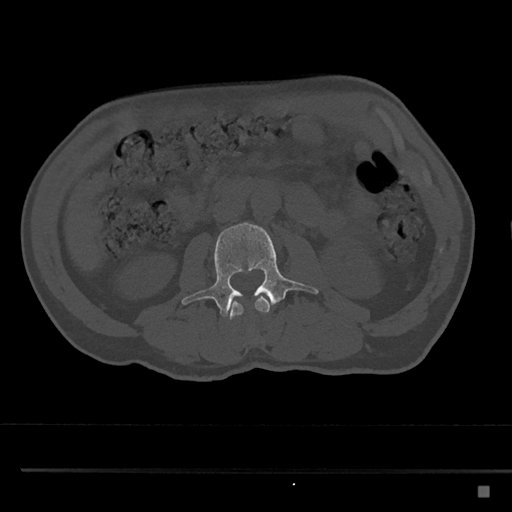
CT including the spine, one axial slice; 120 kVp; bone window (W 1800 / L 400 HU); 0.5 mm slice thickness; 512 × 512 image matrix, field of view 391 × 391 mm. Patient: male, 59 years. Case-level facts recorded for this patient, not image findings: primary cancer: prostate.
Annotated regions visible in this slice (semi-automatic segmentation, software-assisted and operator-edited):
- L2 vertebra: bounding box [x1, y1, x2, y2] px = [228, 296, 270, 320]
- L3 vertebra: [181, 222, 319, 317]